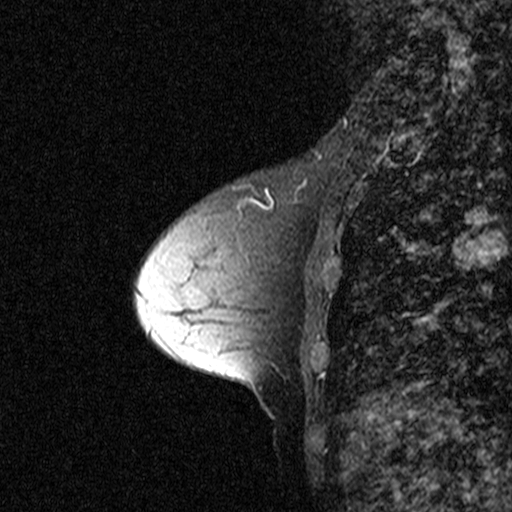
Breast MRI (dynamic contrast-enhanced), one sagittal slice. Position 19 of 44 along the scan axis. Dynamic contrast-enhanced study with each time point stored as its own series, time point 2 of 3 at this slice position (early post-contrast, ordered by acquisition time). 1.5 T. TE 4.5 ms, TR 11 ms. 512 × 512 image matrix, field of view 200 × 200 mm. Patient: female, 53 years. Case-level facts recorded for this patient, not image findings: setting: breast cancer imaged before/during neoadjuvant chemotherapy; receptor status: HR-positive, HER2-negative.
Outlined on this slice (semi-automatically segmented with operator editing):
- analysis volume of interest (the breast-tissue region the enhancement analysis was run in; not a lesion): bounding box <200,178,317,309> (left, top, right, bottom; pixels)
- tumour enhancement mask (voxels above the 90 % enhancement threshold inside the analysis volume of interest): <248,189,273,209>